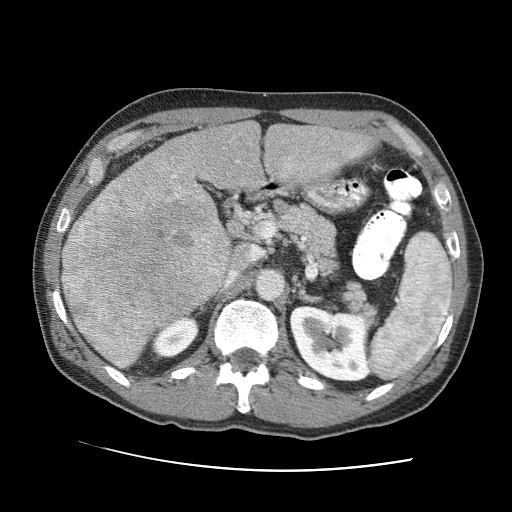
Contrast-enhanced abdominal CT (liver protocol), one axial slice. Position 43 of 95 along the scan axis. One of 2 acquisitions stored at this slice position. Soft-tissue window (W 400 / L 40 HU). 2.5 mm slice thickness. 512 × 512 image matrix, field of view 360 × 360 mm. From the clinical record (not read from this slice): diagnosis: hepatocellular carcinoma (patient treated with transarterial chemoembolisation; whether this scan precedes or follows treatment is not stated here); TNM stage (as recorded): Stage-IVA; Child-Pugh class: A.
Structures marked on this image (semi-automatically segmented with operator editing):
- liver parenchyma outside the tumour (the mass and vessels are separate outlines, so this box may not span the whole liver): bounding box <88,122,374,326> (left, top, right, bottom; pixels)
- mass: <62,175,233,368>
- liver vessels: <128,142,360,180>